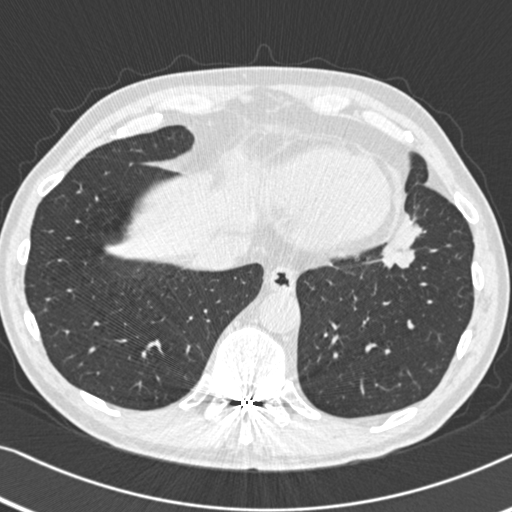
Low-dose screening chest CT, one axial slice. Slice 124 of 383 in the series (ordered by position). Reconstruction kernel B30f. 120 kVp. Lung window (W 1500 / L -600 HU). 1 mm slice thickness. 512 × 512 image matrix.
Annotated regions visible in this slice (outlined manually by an expert reader):
- lesion 1 (tumor, upper lobe of left lung): bounding box <382,217,425,268> (left, top, right, bottom; pixels)